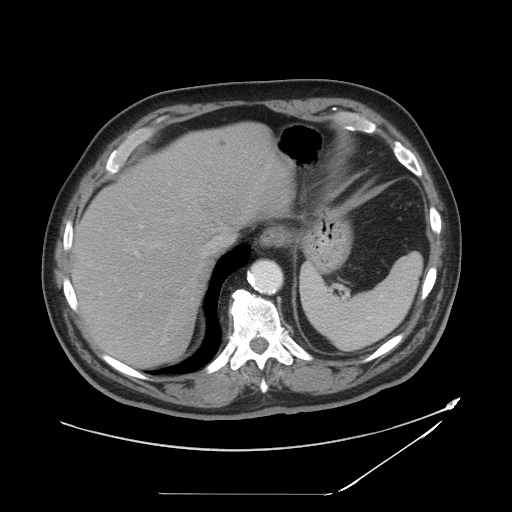
Contrast-enhanced abdominal CT, one axial slice; slice 36 of 49 in the series (ordered by position); 120 kVp; intravenous contrast given; soft-tissue window (W 400 / L 40 HU); 5 mm slice thickness; 512 × 512 image matrix, field of view 461 × 461 mm. Male patient, age 72 years. Case-level facts recorded for this patient, not image findings: diagnosis: colorectal cancer liver metastases, imaged before liver resection; multiple liver metastases: no; largest metastasis: 2.5 cm; disease in both lobes: no.
Outlined on this slice (manually delineated by an expert):
- hepatic veins: bounding box [x1, y1, x2, y2] px = [150, 236, 222, 258]
- liver: [77, 124, 287, 366]
- planned liver remnant (the part of the liver to remain after resection): [77, 180, 212, 366]
- portal vein (with intrahepatic branches): [139, 151, 247, 297]